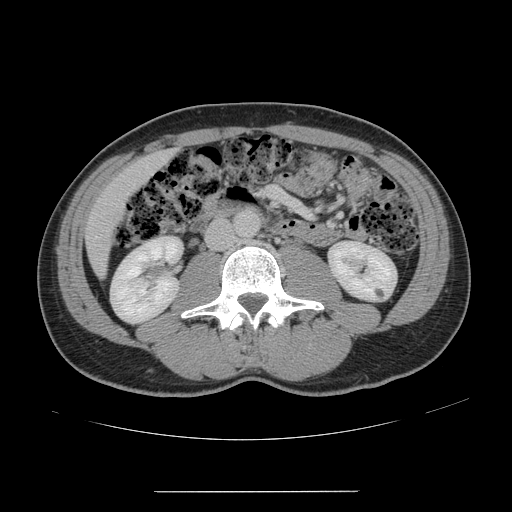
Contrast-enhanced abdominal CT, one axial slice; slice 40 of 178 in the series (ordered by position); 120 kVp; intravenous contrast given; soft-tissue window (W 400 / L 40 HU); 2.5 mm slice thickness; 512 × 512 image matrix, field of view 401 × 401 mm. Male patient, age 53 years. From the clinical record (not read from this slice): diagnosis: colorectal cancer liver metastases, imaged before liver resection; multiple liver metastases: yes; largest metastasis: 2.4 cm; disease in both lobes: no.
Outlined on this slice (outlined manually by an expert reader):
- liver: bounding box (x1, y1, x2, y2) in pixels: (86, 152, 172, 273)